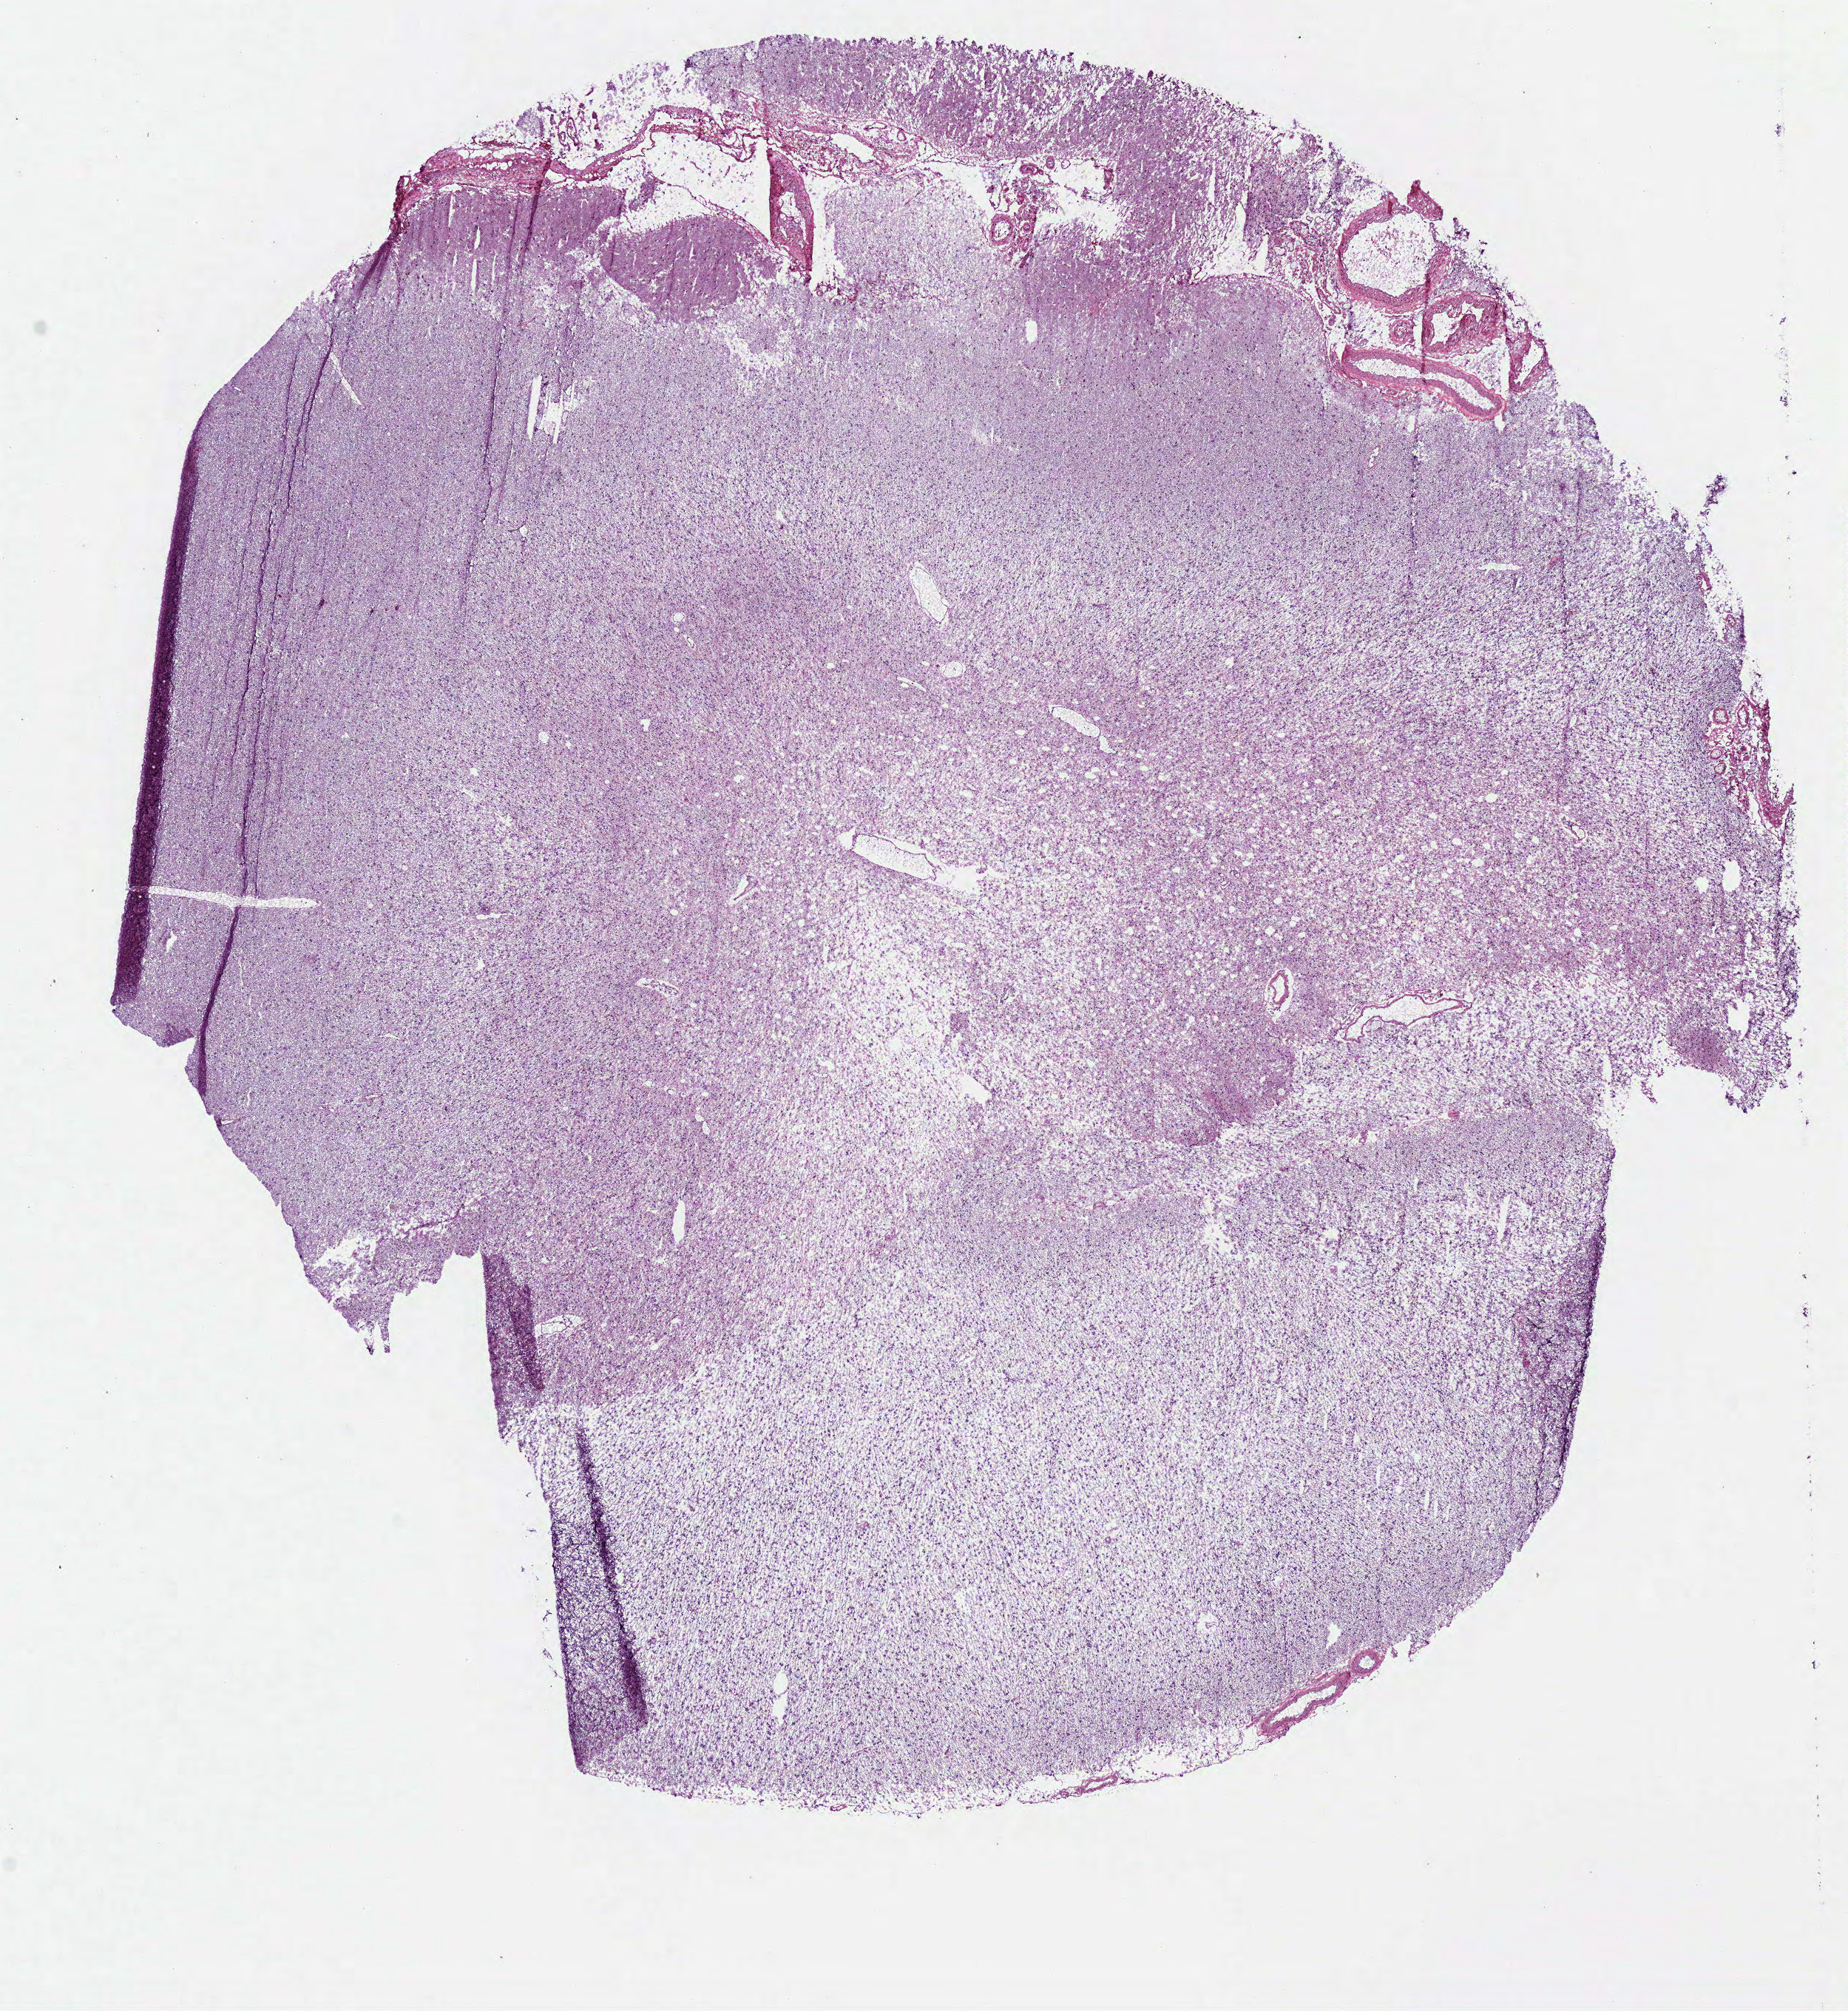
Whole-slide histology image, Hematoxylin and eosin (H&E) stained — whole scanned area (about 9.8 x 10.7 mm, acquisition: 40x scan) shown as a low-resolution overview; frozen section; primary tumour sample from the brain. Patient: male, age at initial diagnosis 48 years. Histologic grade: G2 (moderately differentiated). Slide review estimates, as recorded: tumour cells 100%, tumour nuclei 75%, normal cells 0%, stromal cells 0%, necrosis 0%.
Pathologic diagnosis: Oligodendroglioma, NOS.